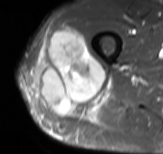
MRI of an extremity soft-tissue mass, one axial slice; slice 39 of 61 in the series (ordered by position); STIR; MR volume resampled by the dataset authors to the PET/CT grid (not the native acquisition matrix); 3.27 mm slice thickness; 163 × 154 image matrix. Male patient. Case-level facts recorded for this patient, not image findings: histological type: poorly differentiated synovial sarcoma; grade: high; site of the primary tumour: right buttock.
Outlined on this slice (expert contour drawn on MRI and transferred to this co-registered scan by the dataset authors):
- gross tumour volume including surrounding oedema: bounding box [x1, y1, x2, y2] px = [36, 27, 106, 115]
- gross tumour volume (mass): [39, 27, 106, 113]